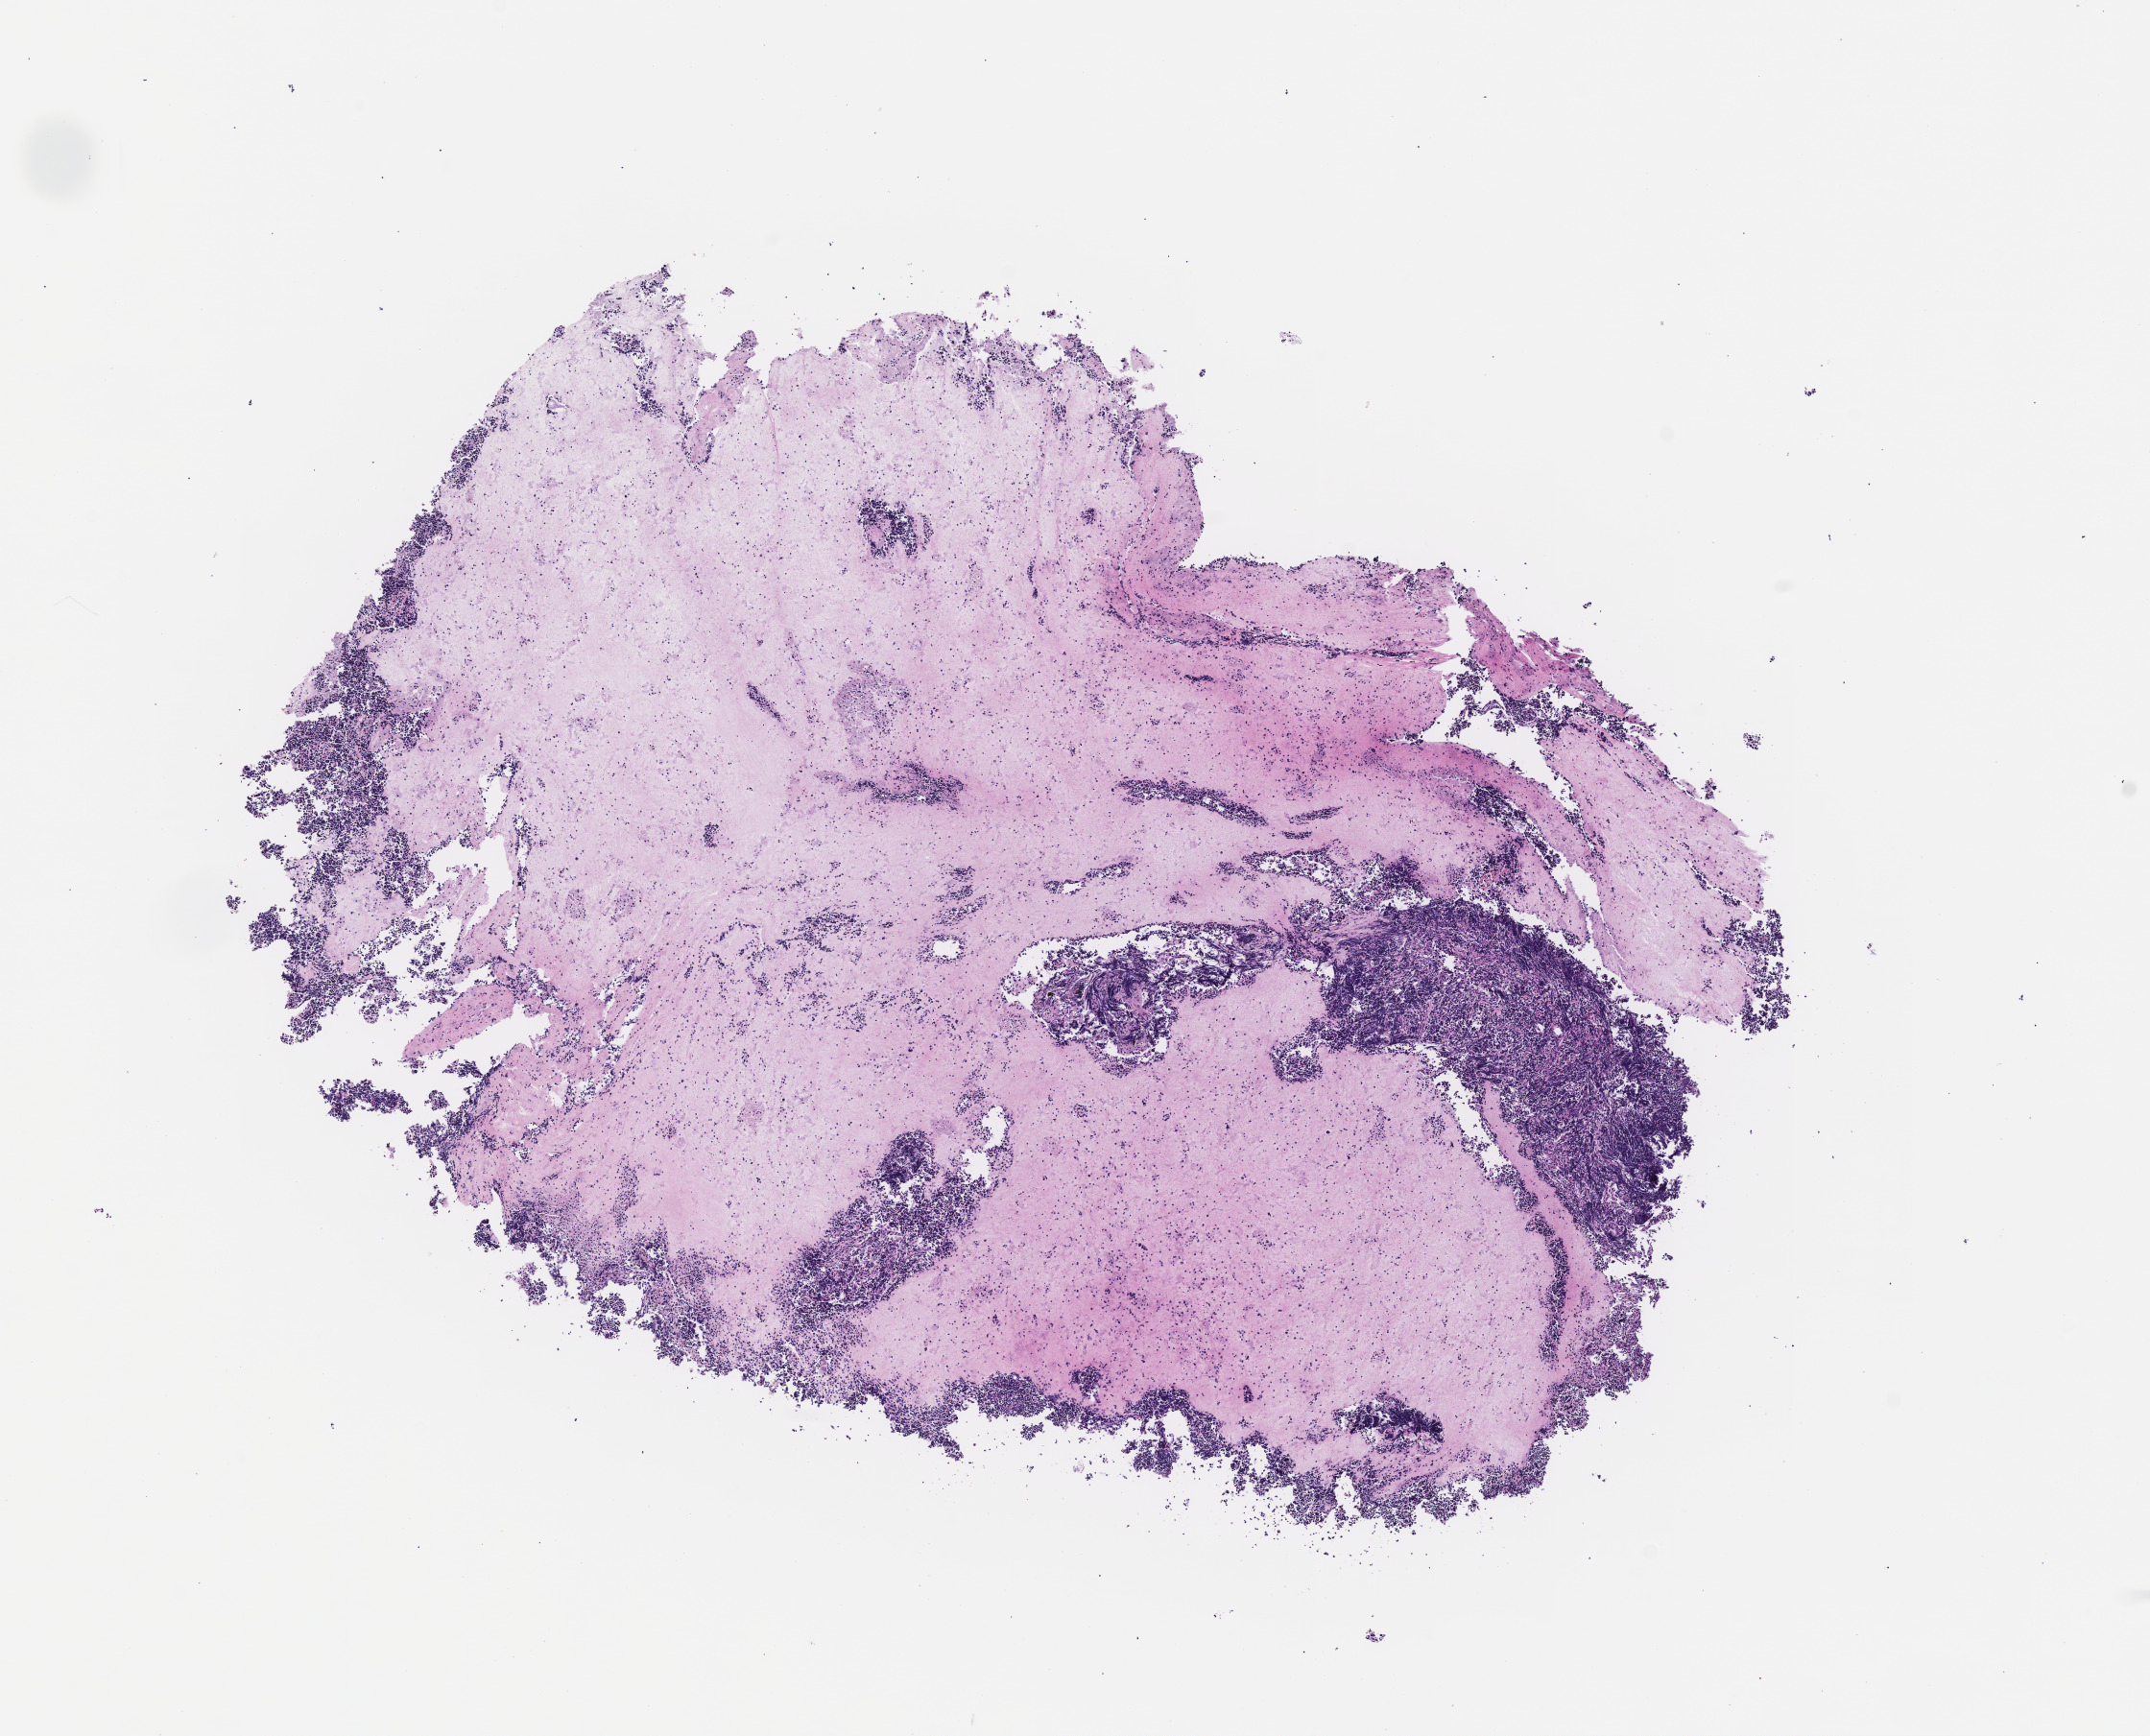
Haematoxylin and eosin whole-slide image — whole scanned area (about 9.0 x 7.3 mm) shown as a low-resolution overview. FFPE section. Site: lung. Specimen time point: archival tissue. Patient sex: male.
This section: primary tumour tissue. Diagnosis: Small Cell Lung Carcinoma.